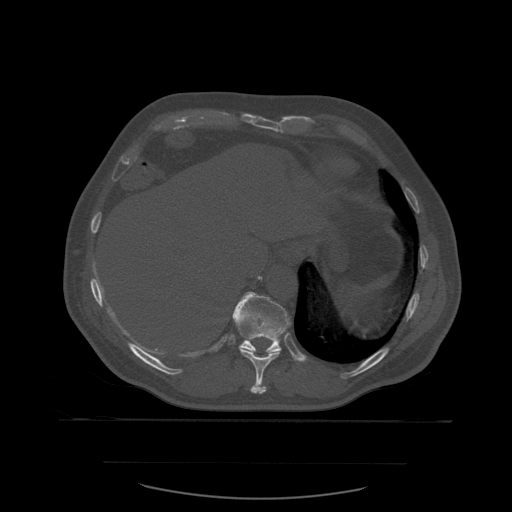
CT including the spine, one axial slice; position 309 of 590 along the scan axis; bone window (W 1800 / L 400 HU); 512 × 512 image matrix, field of view 479 × 479 mm. Patient age 71 years. Case-level facts recorded for this patient, not image findings: primary cancer: lung.
Outlined on this slice (semi-automatically segmented with operator editing):
- T10 vertebra: bounding box <237,306,285,394> (left, top, right, bottom; pixels)
- T11 vertebra: <232,292,291,354>